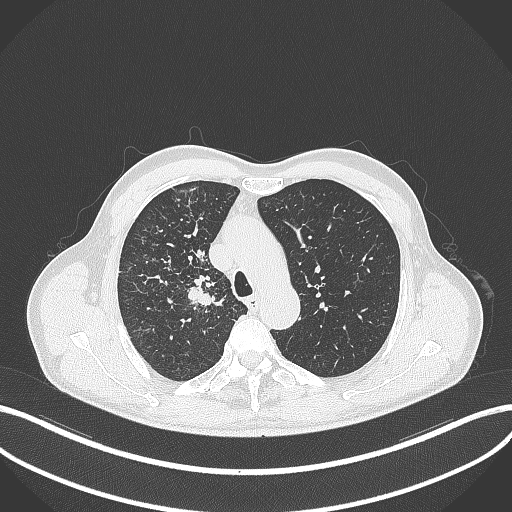
Chest CT, one axial slice; slice 357 of 490 in the series (ordered by position); reconstruction kernel B70f; lung window (W 1500 / L -600 HU); 1 mm slice thickness; 512 × 512 image matrix. Patient: male, 69 years. Case-level facts recorded for this patient, not image findings: clinical TNM (as recorded): T2a N0 M0.
Structures marked on this image (bounding box drawn by a radiologist):
- lung tumour (recorded histology: adenocarcinoma): bounding box (x1, y1, x2, y2) in pixels: (185, 271, 226, 314)